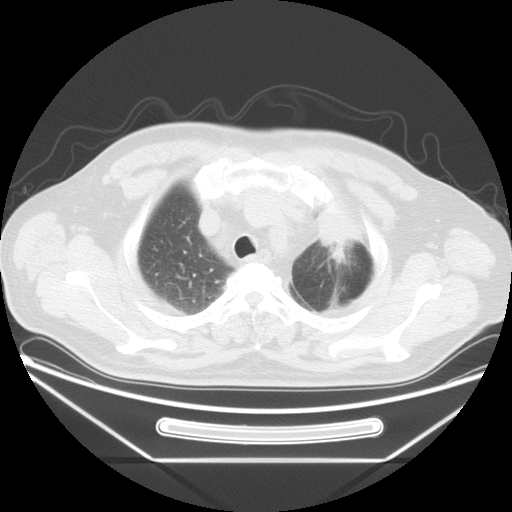
Chest CT, one axial slice. Slice 33 of 38 in the series (ordered by position). Lung window (W 1500 / L -600 HU). 5 mm slice thickness. 512 × 512 image matrix. Male patient, age 61 years. Case-level facts recorded for this patient, not image findings: clinical TNM (as recorded): T2a N0 M0.
Annotated regions visible in this slice (rectangle marked by the reading radiologist):
- lung tumour (recorded histology: small cell carcinoma): box from (x=313, y=198) to (x=365, y=270) px